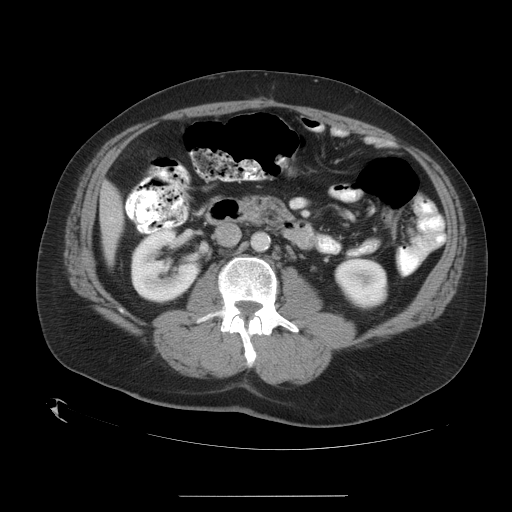
Contrast-enhanced abdominal CT, one axial slice; position 9 of 35 along the scan axis; reconstruction kernel STANDARD; intravenous contrast given; soft-tissue window (W 400 / L 40 HU); 7.5 mm slice thickness; 512 × 512 image matrix, field of view 450 × 450 mm. Male patient, age 67 years. Case-level facts recorded for this patient, not image findings: diagnosis: colorectal cancer liver metastases, imaged before liver resection; multiple liver metastases: no; largest metastasis: 2.3 cm.
Annotated regions visible in this slice (outlined manually by an expert reader):
- liver: bounding box [x1, y1, x2, y2] px = [101, 187, 122, 254]
- planned liver remnant (the part of the liver to remain after resection): [101, 187, 122, 255]